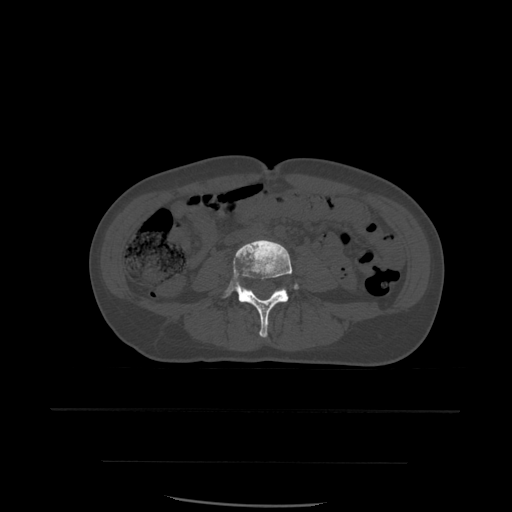
CT including the spine, one axial slice; slice 171 of 574 in the series (ordered by position); bone window (W 1800 / L 400 HU); 512 × 512 image matrix, field of view 392 × 392 mm. Patient age 48 years. From the clinical record (not read from this slice): primary cancer: lung.
Outlined on this slice (semi-automatic segmentation, software-assisted and operator-edited):
- L4 vertebra: bounding box (x1, y1, x2, y2) in pixels: (221, 240, 300, 338)